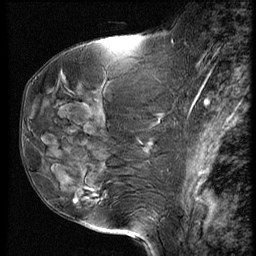
Breast MRI (dynamic contrast-enhanced), one sagittal slice; position 26 of 60 along the scan axis; dynamic contrast-enhanced series, image 2 of 4 at this slice position (ordered by acquisition); 1.5 T; TE 4.2 ms, TR 9 ms; 2.5 mm slice thickness; 256 × 256 image matrix, field of view 180 × 180 mm. Patient: female, 50 years. Case-level facts recorded for this patient, not image findings: setting: breast cancer imaged before/during neoadjuvant chemotherapy; receptor status: HR-positive, HER2-negative.
Structures marked on this image (semi-automatic segmentation, software-assisted and operator-edited):
- analysis volume of interest (the breast-tissue region the enhancement analysis was run in; not a lesion): bounding box (x1, y1, x2, y2) in pixels: (48, 109, 135, 230)
- tumour enhancement mask (voxels above the 140 % enhancement threshold inside the analysis volume of interest): (92, 190, 94, 192)